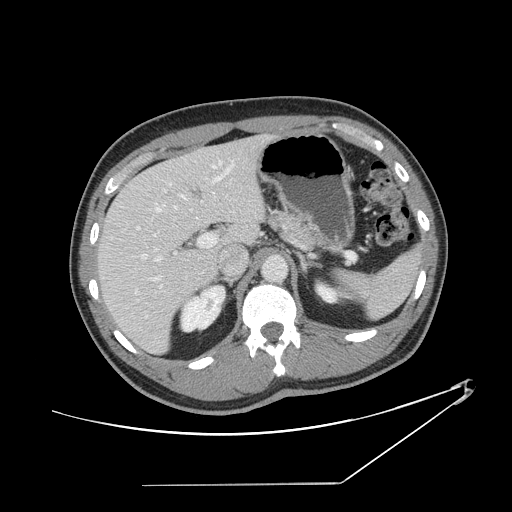
Contrast-enhanced abdominal CT, one axial slice; position 88 of 152 along the scan axis; intravenous contrast given; soft-tissue window (W 400 / L 40 HU); 512 × 512 image matrix, field of view 432 × 432 mm. Male patient, age 45 years. Case-level facts recorded for this patient, not image findings: diagnosis: colorectal cancer liver metastases, imaged before liver resection; multiple liver metastases: no.
Outlined on this slice (expert manual segmentation):
- hepatic veins: box from (x=111, y=160) to (x=223, y=294) px
- liver: (x=99, y=136)–(x=265, y=353)
- planned liver remnant (the part of the liver to remain after resection): (x=99, y=156)–(x=225, y=352)
- portal vein (with intrahepatic branches): (x=137, y=163)–(x=234, y=318)